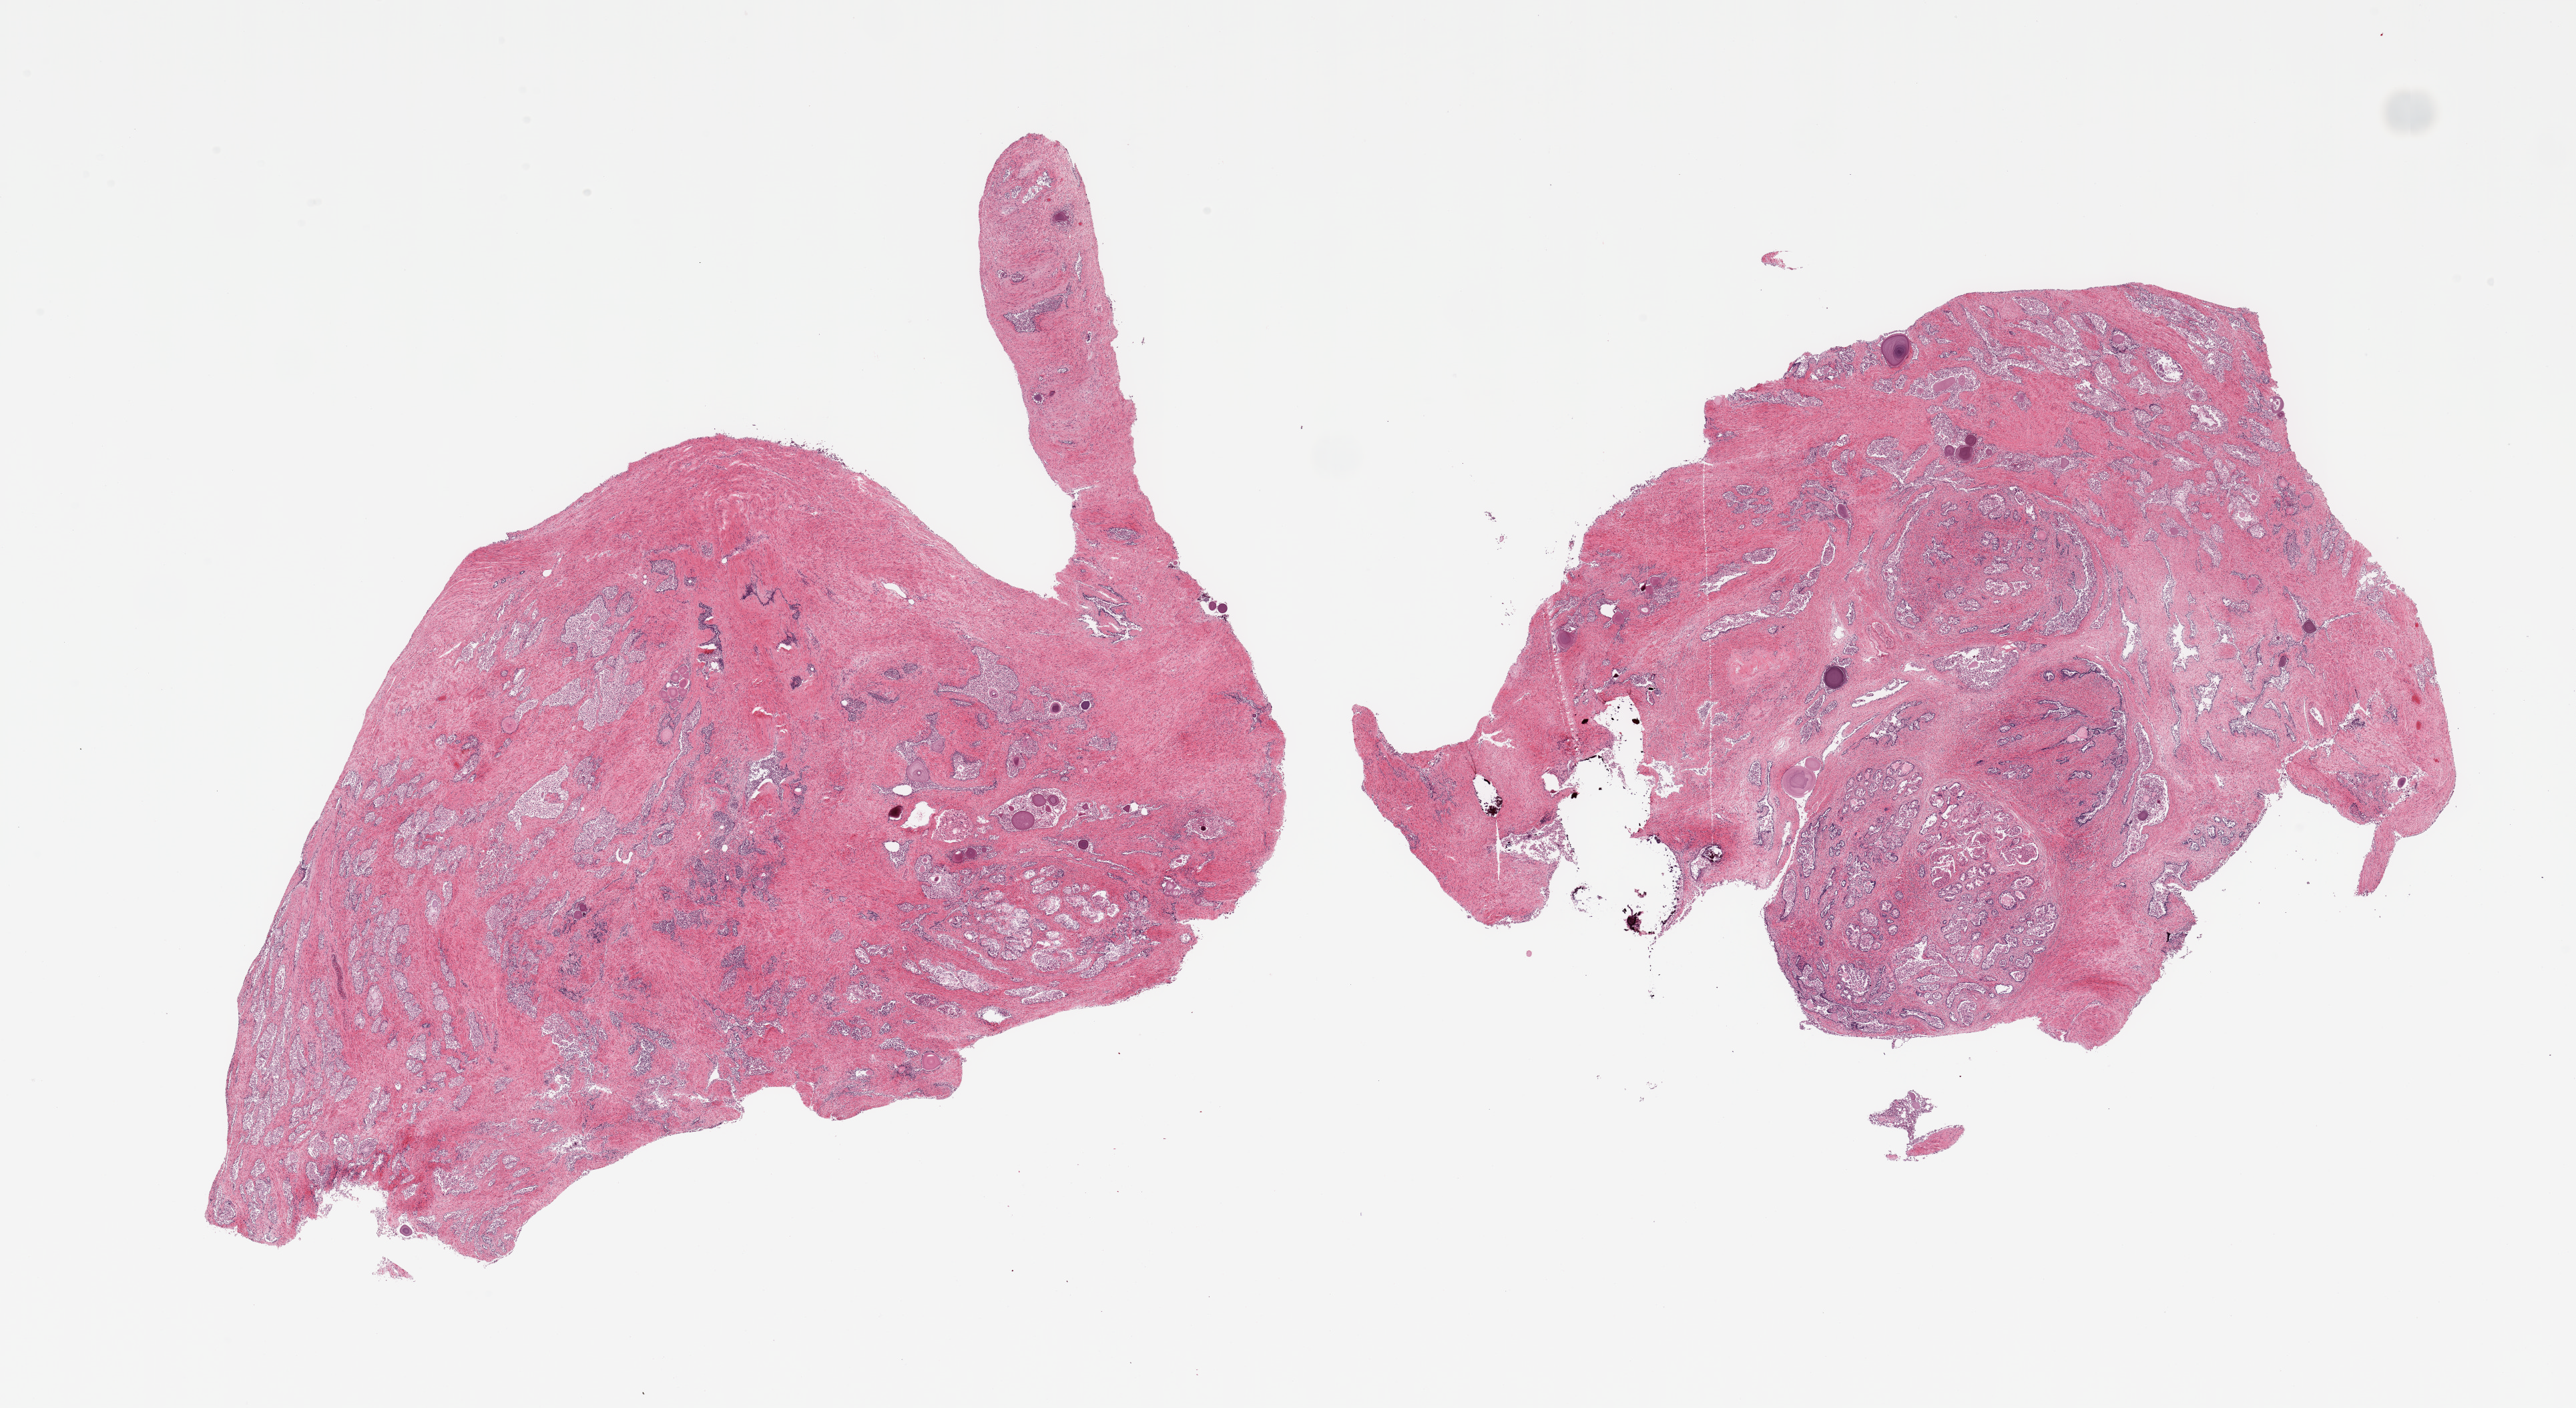
Whole-slide image, H&E stain, shown as a low-resolution overview of the whole scanned area (about 30.5 x 16.7 mm); PAXgene-fixed, paraffin-embedded tissue; sampled site (target tissue): prostate; donor tissue sample.
Reviewer comment on this tissue sample: 2 pieces; fibromuscular stroma and autolyzed glandular structures, with scattered corpora amylacea.